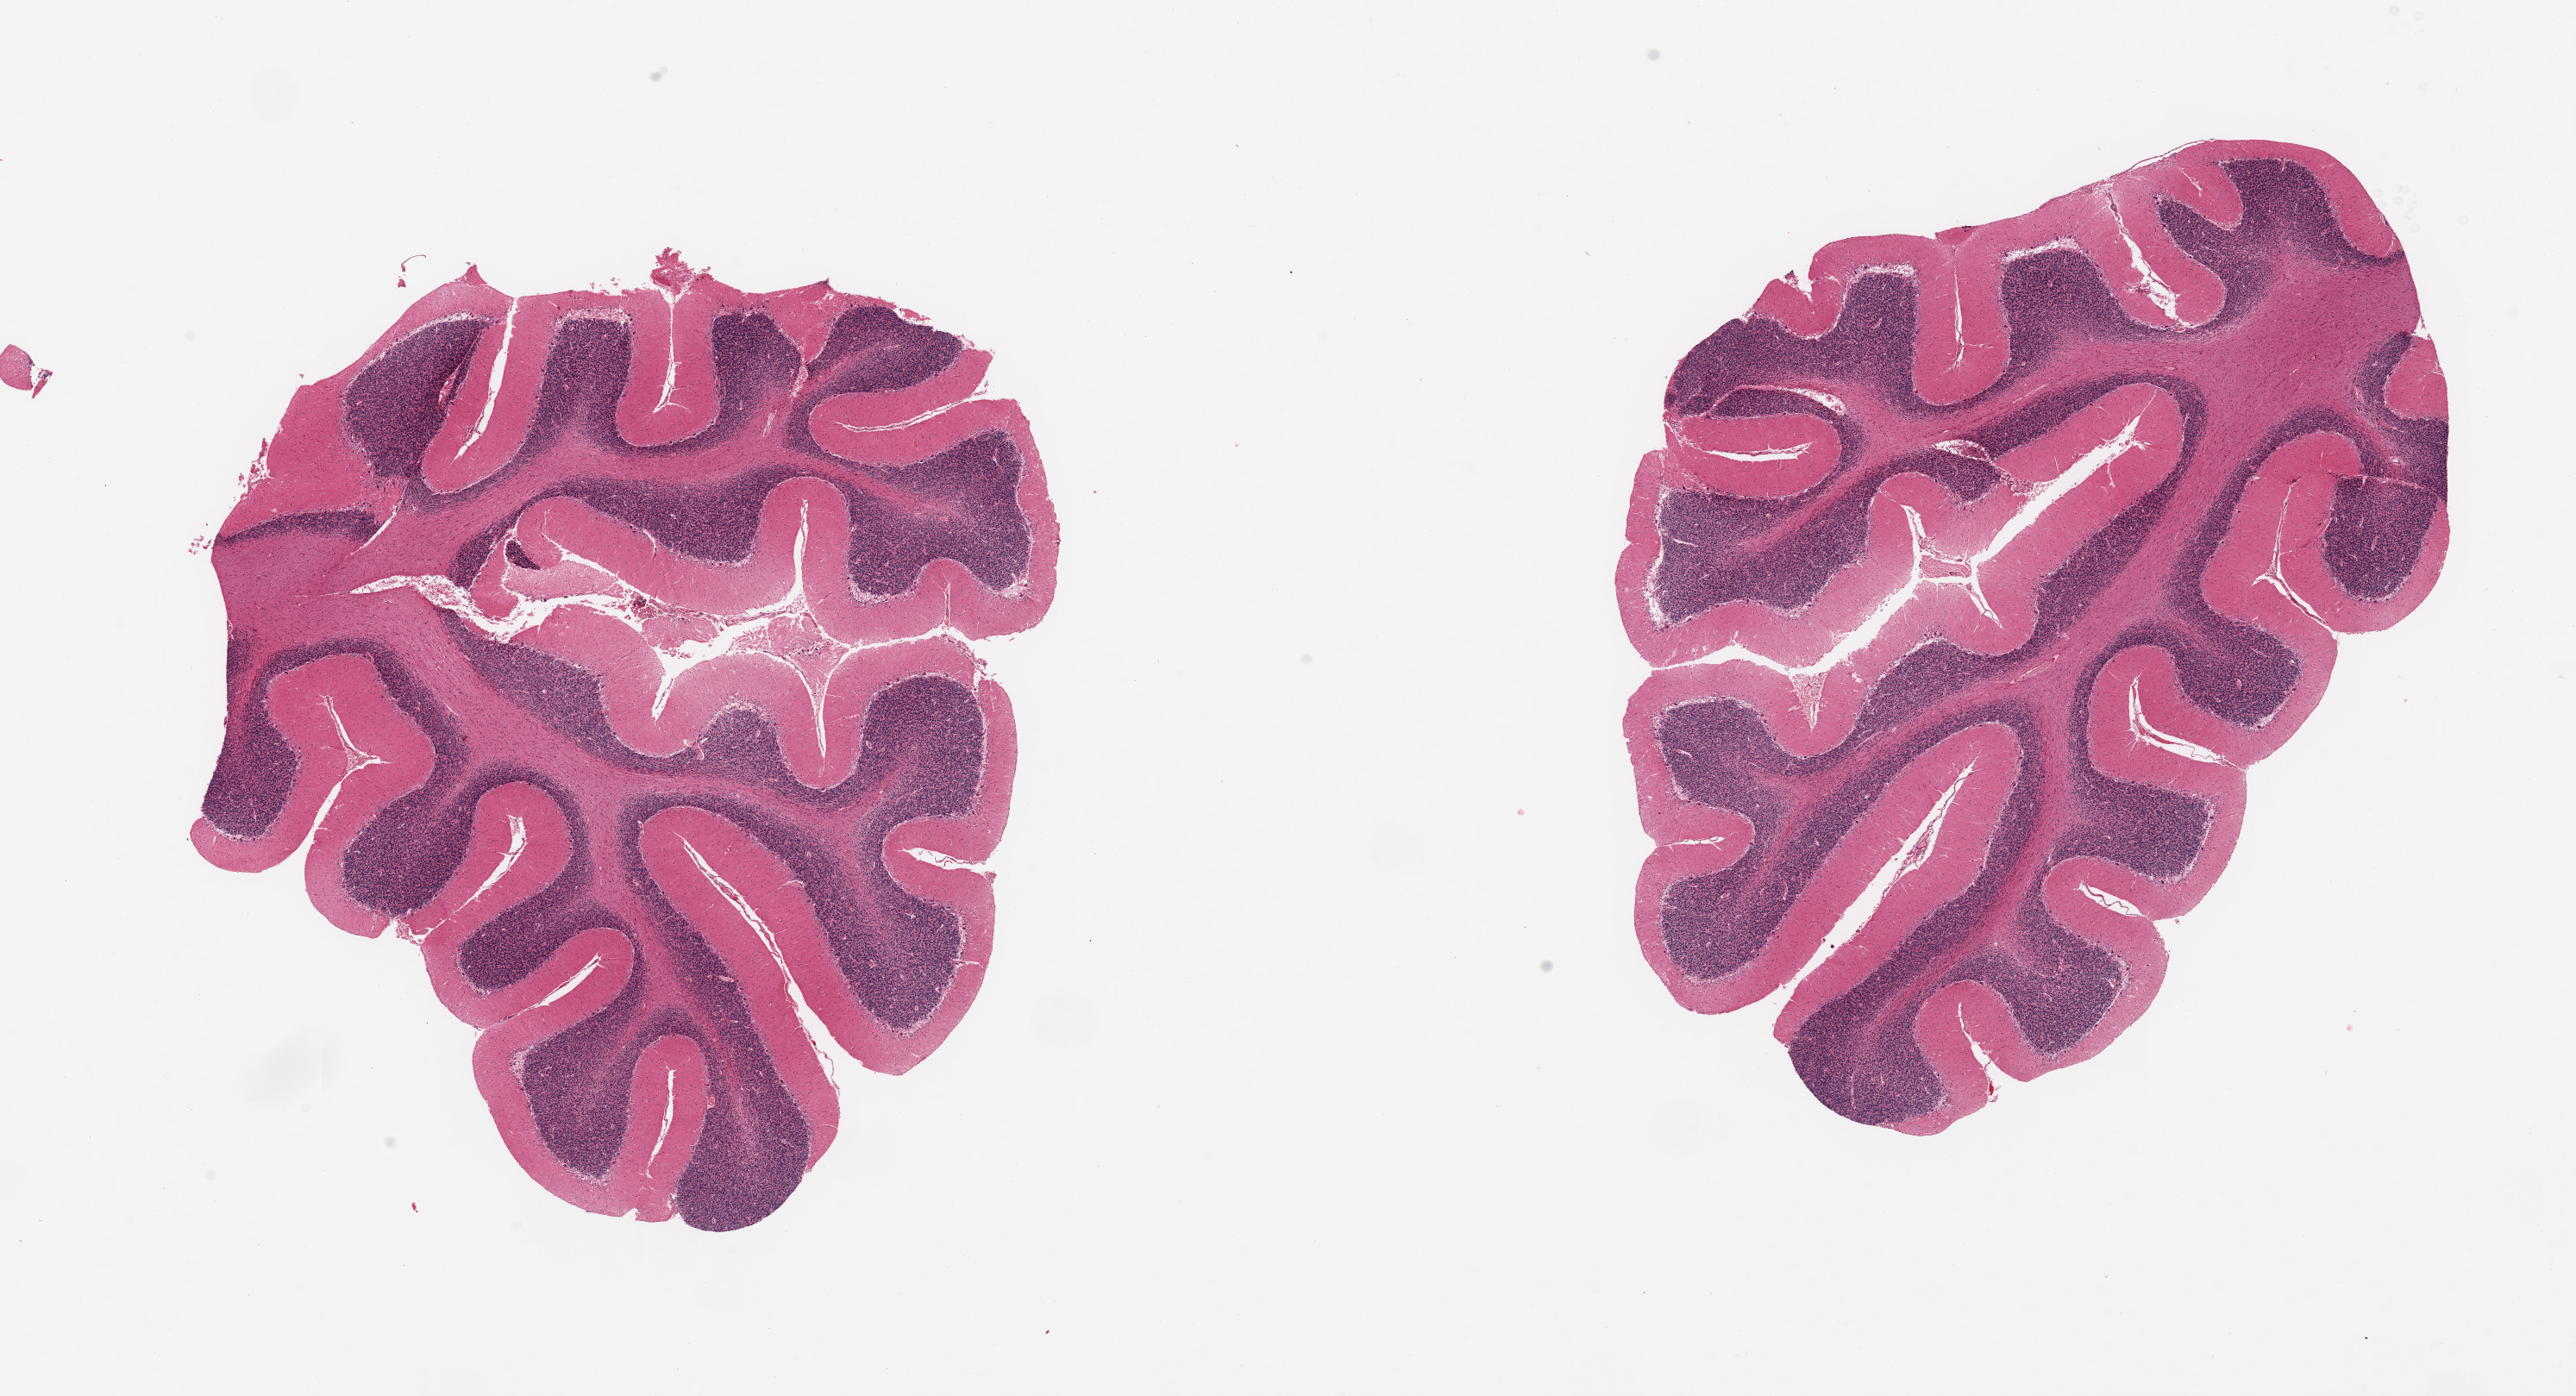
H&E whole-slide image — low-resolution overview of the scanned area, about 23.6 x 12.8 mm, PAXgene-fixed, paraffin-embedded tissue, section of cerebellum (target tissue), tissue donor sample.
Pathologist's review note for this sample: 2 pieces.